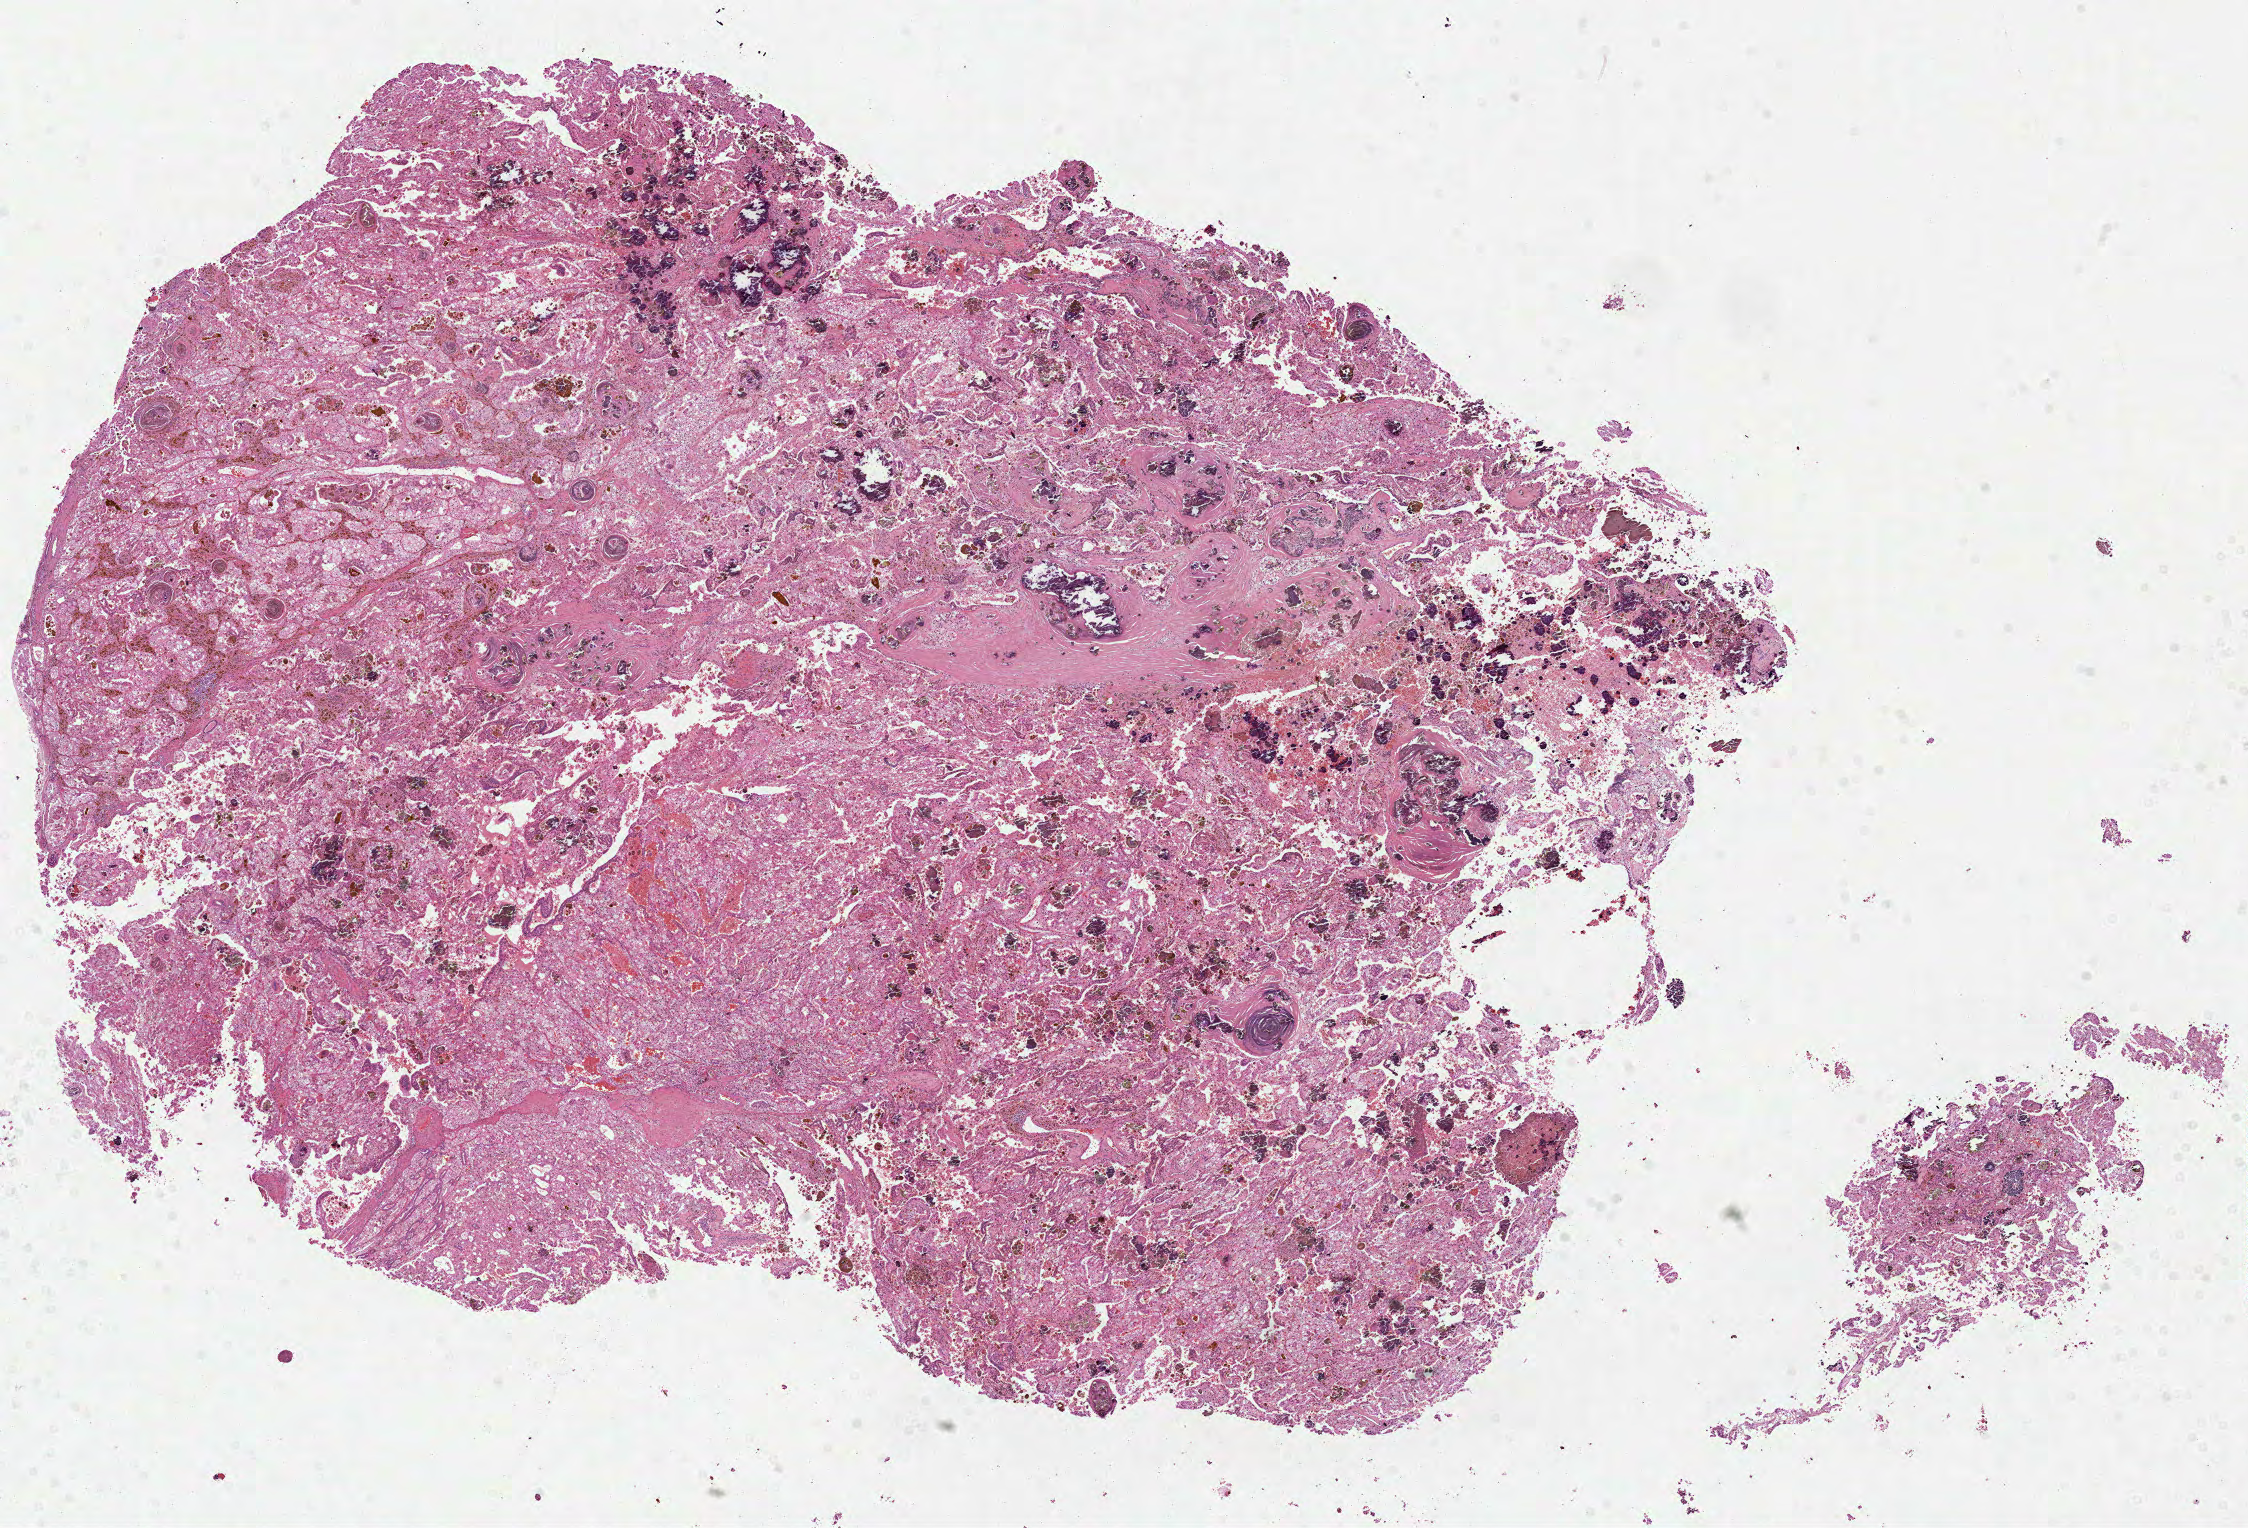
Whole-slide histology image, H&E — shown as a low-resolution overview of the whole scanned area (about 18.1 x 12.3 mm); formalin-fixed paraffin-embedded (FFPE) diagnostic section; primary tumour sample from the kidney. Female, age 51 years at initial diagnosis. Histologic grade: G2 (moderately differentiated).
Diagnosis: Clear cell adenocarcinoma, NOS. AJCC pathologic stage: I. TNM: T1b N0 M0.